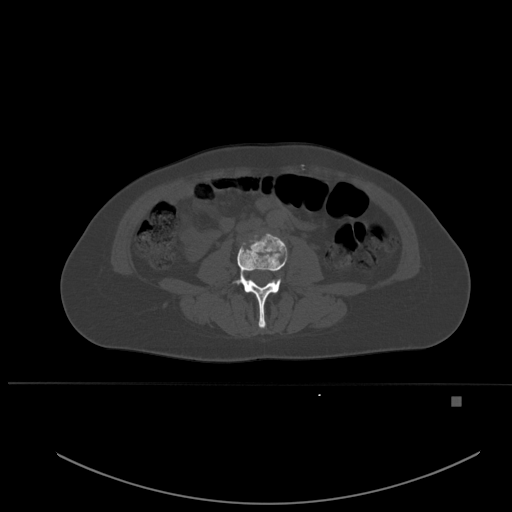
CT including the spine, one axial slice. Position 190 of 651 along the scan axis. Bone window (W 1800 / L 400 HU). 512 × 512 image matrix. Female patient, age 49 years. Case-level facts recorded for this patient, not image findings: primary cancer: breast; vertebrae with lytic lesions (as recorded): L3, T12, L4.
Outlined on this slice (semi-automatically segmented with operator editing):
- L3 vertebra: bounding box [x1, y1, x2, y2] px = [233, 233, 289, 328]